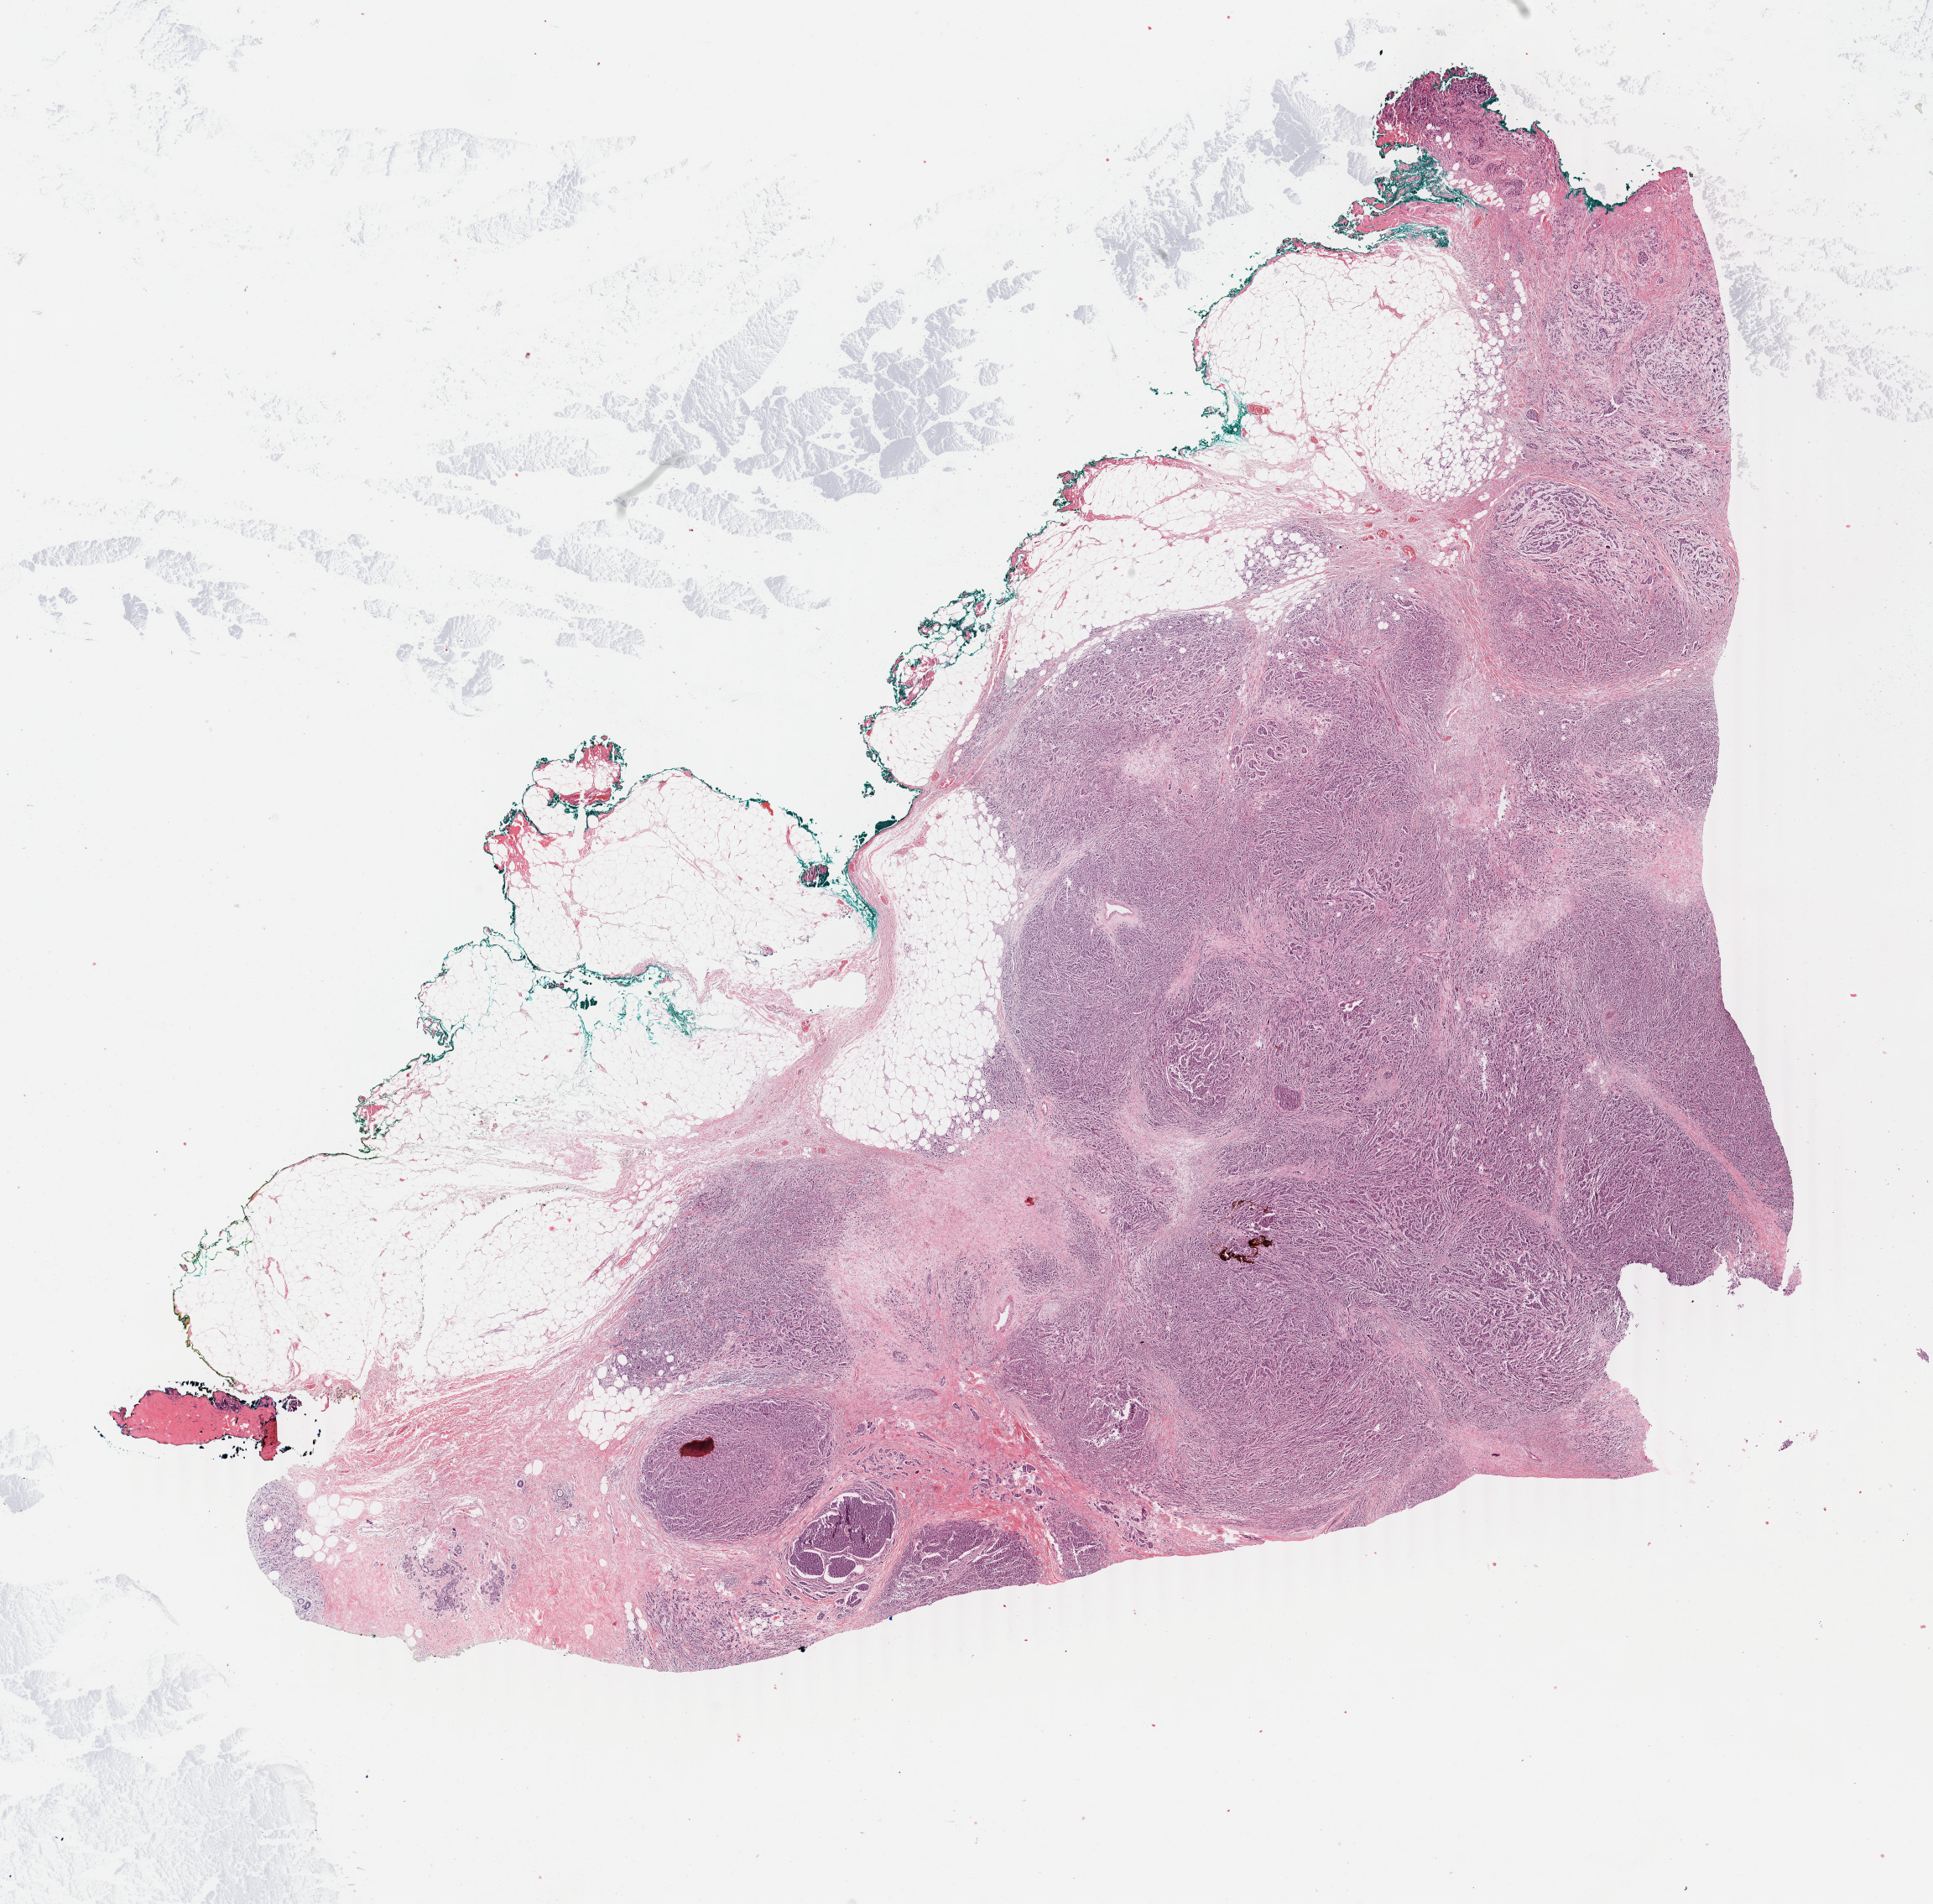
Whole-slide histology image, H&E, a low-resolution overview of the entire scanned area, about 18.3 x 18.1 mm (slide scanned at 40x), FFPE section, sample: primary tumour, breast. Female patient; age at initial diagnosis 61 years.
AJCC pathologic stage: IIIA (6th edition). Histologic diagnosis: Infiltrating duct carcinoma, NOS.